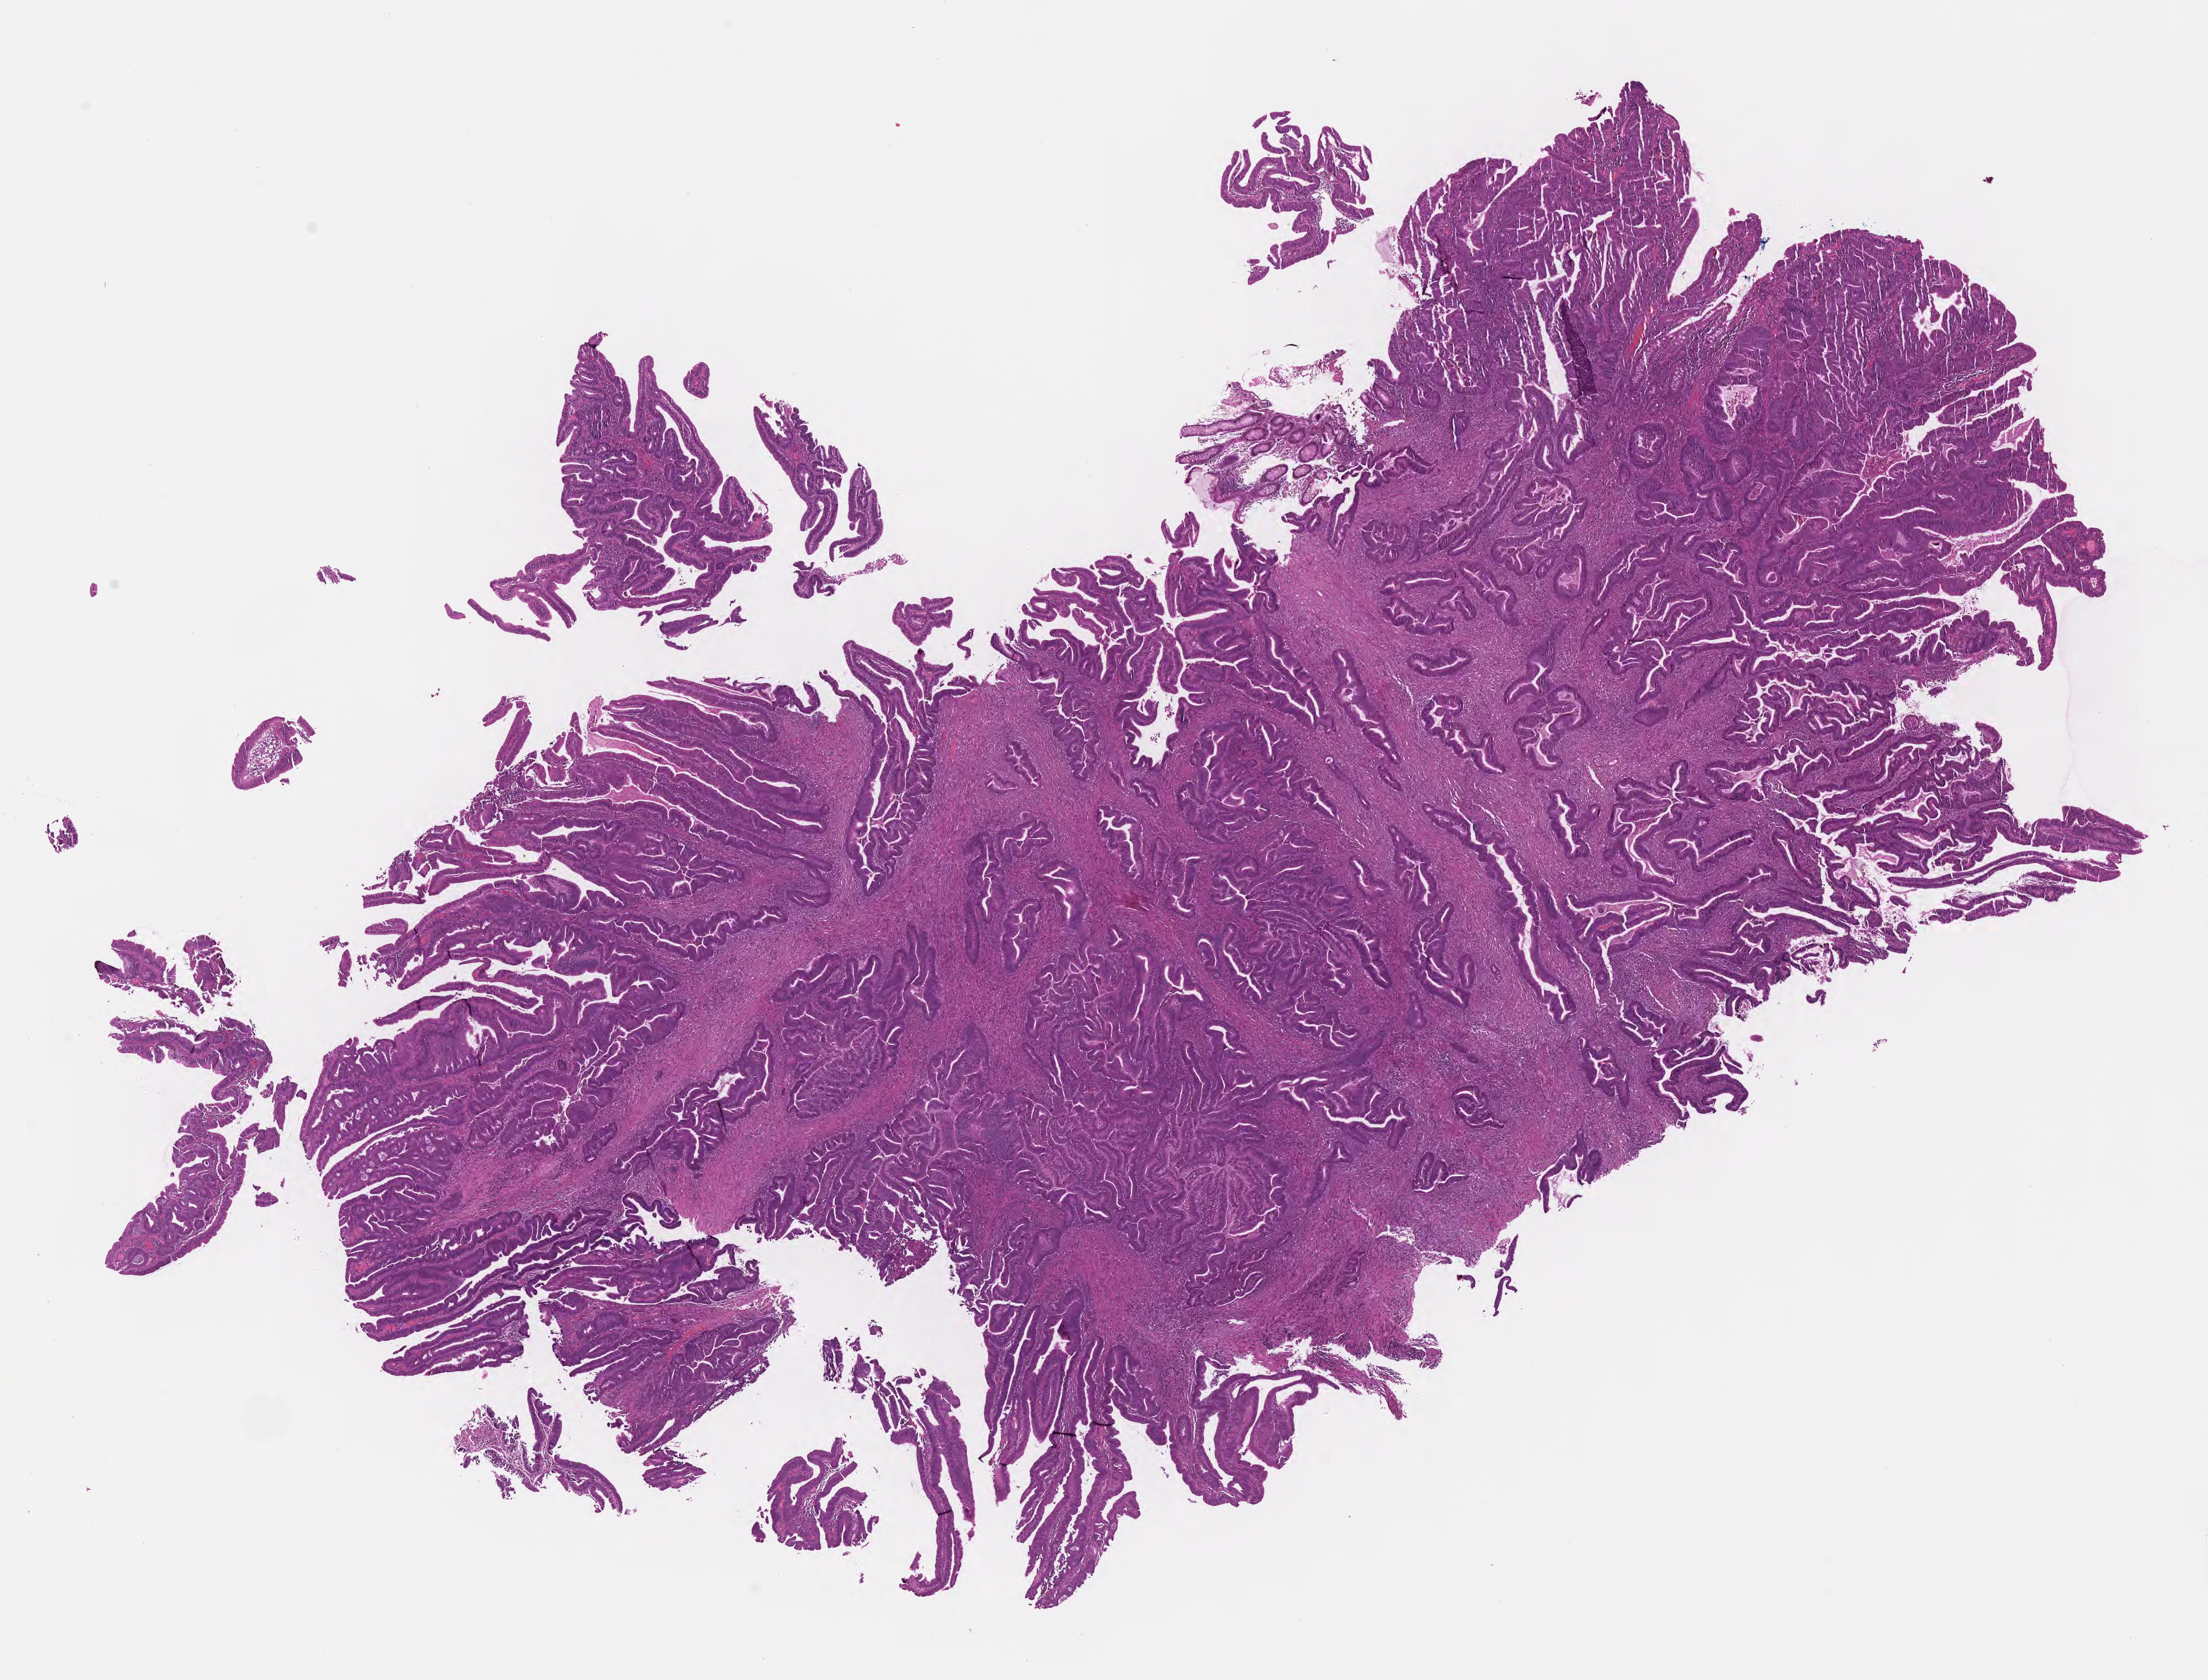
Whole-slide image, haematoxylin and eosin stain, a low-resolution overview of the entire scanned area, about 16.1 x 12.3 mm; formalin-fixed, paraffin-embedded (FFPE) tissue; specimen: primary tumor; site: ascending colon. Patient: male, age at initial diagnosis 61 years. Tumor grade: GB (borderline). Pathologist review of this section (percent, as recorded): tumor cells 50%, tumor nuclei 70%, stromal cells 50%, necrosis 0%, normal cells 0%. Infiltration values recorded for this section: lymphocyte infiltration 0%, monocyte infiltration 0%, neutrophil infiltration 0%.
* AJCC pathologic stage: Stage I
* histologic diagnosis: Adenocarcinoma, NOS
* section: bottom of the tissue portion